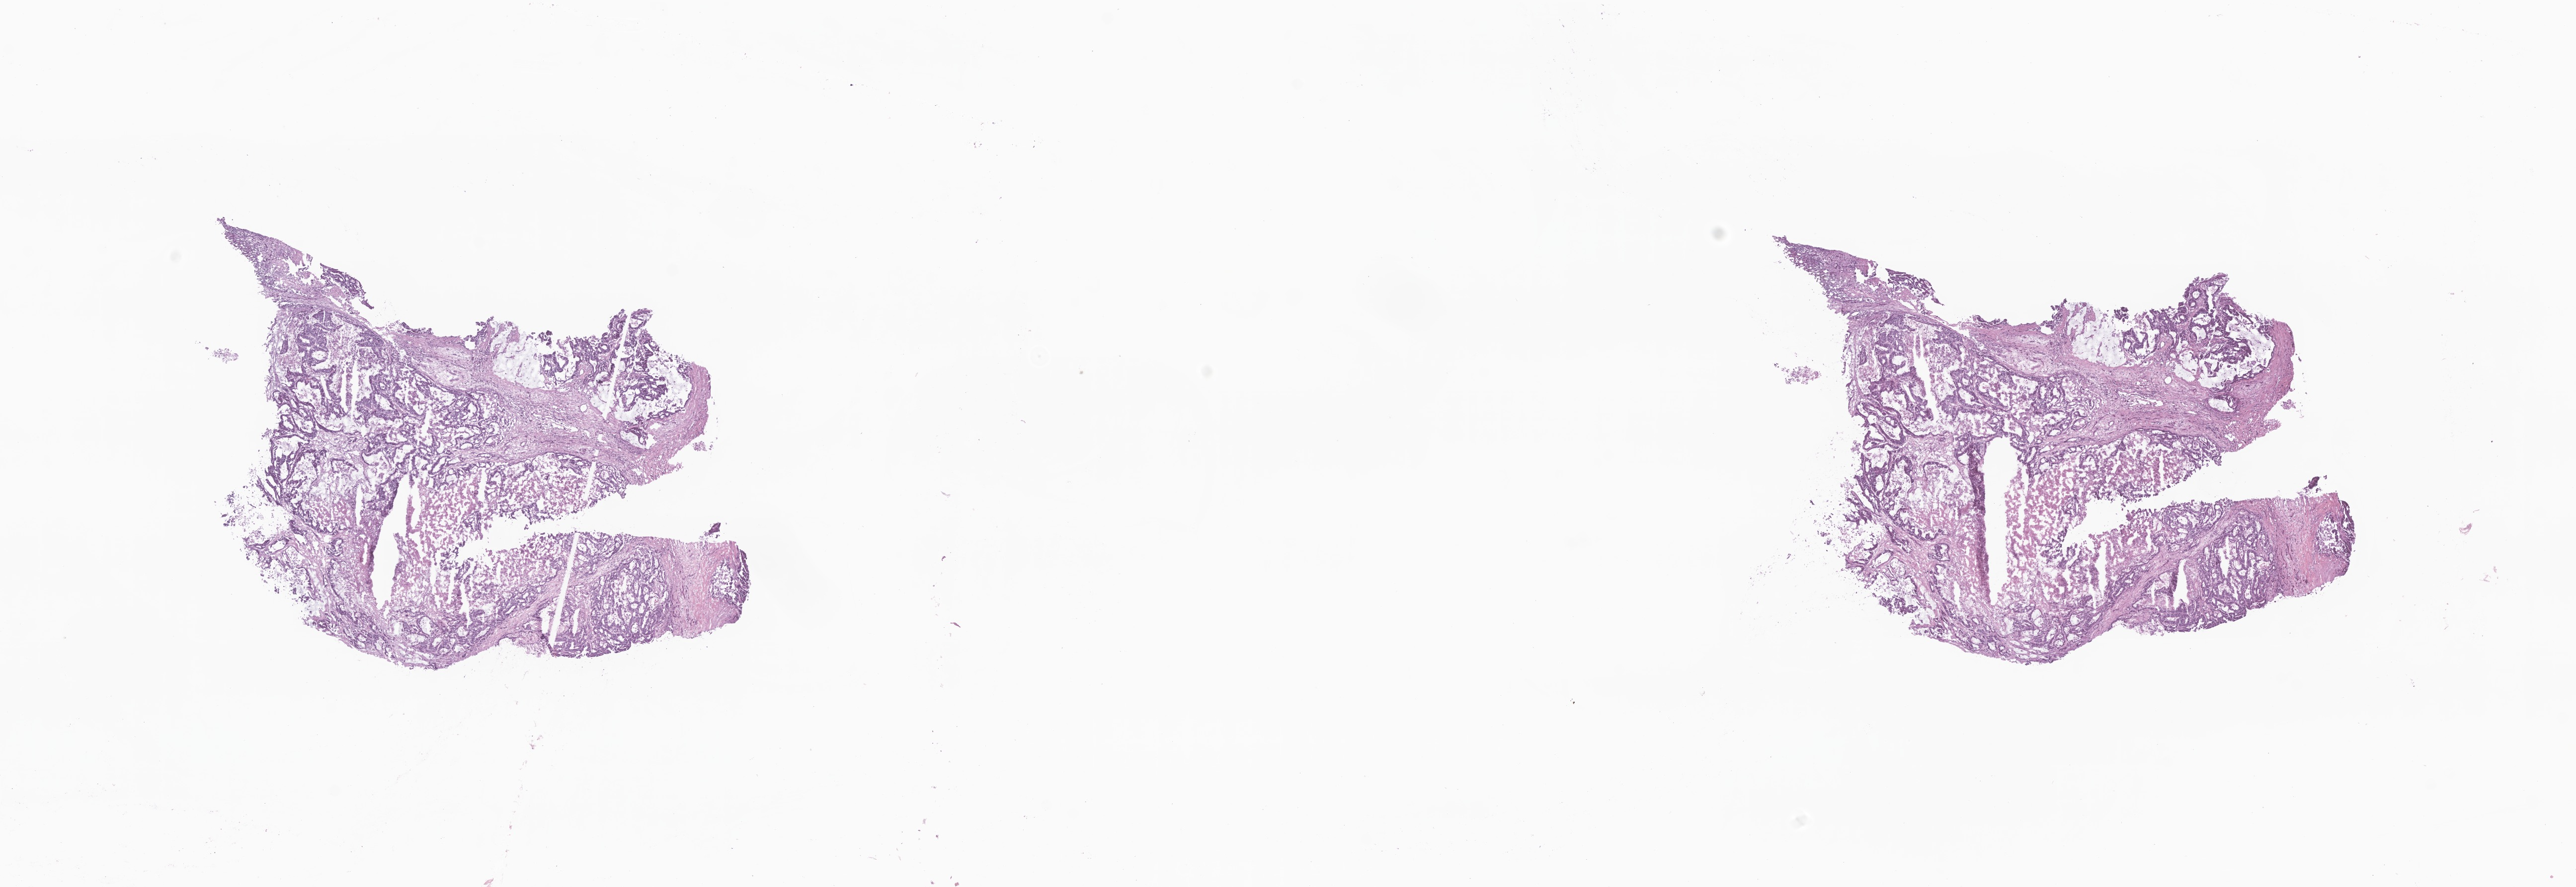
Haematoxylin and eosin whole-slide image — shown as a low-resolution overview of the whole scanned area (about 21.9 x 7.5 mm), frozen section, specimen: metastatic tumor tissue, resected from liver. Patient: male, age at initial diagnosis 72 years. Slide review estimates, as recorded: tumor cells 75%, tumor nuclei 75%, stromal cells 15%, necrosis 10%, normal cells 0%. Inflammatory infiltration, as recorded: lymphocyte infiltration 3%, monocyte infiltration 2%, neutrophil infiltration 5%.
Patient diagnosis (primary): Adenocarcinoma, NOS. Section: top of the tissue portion.